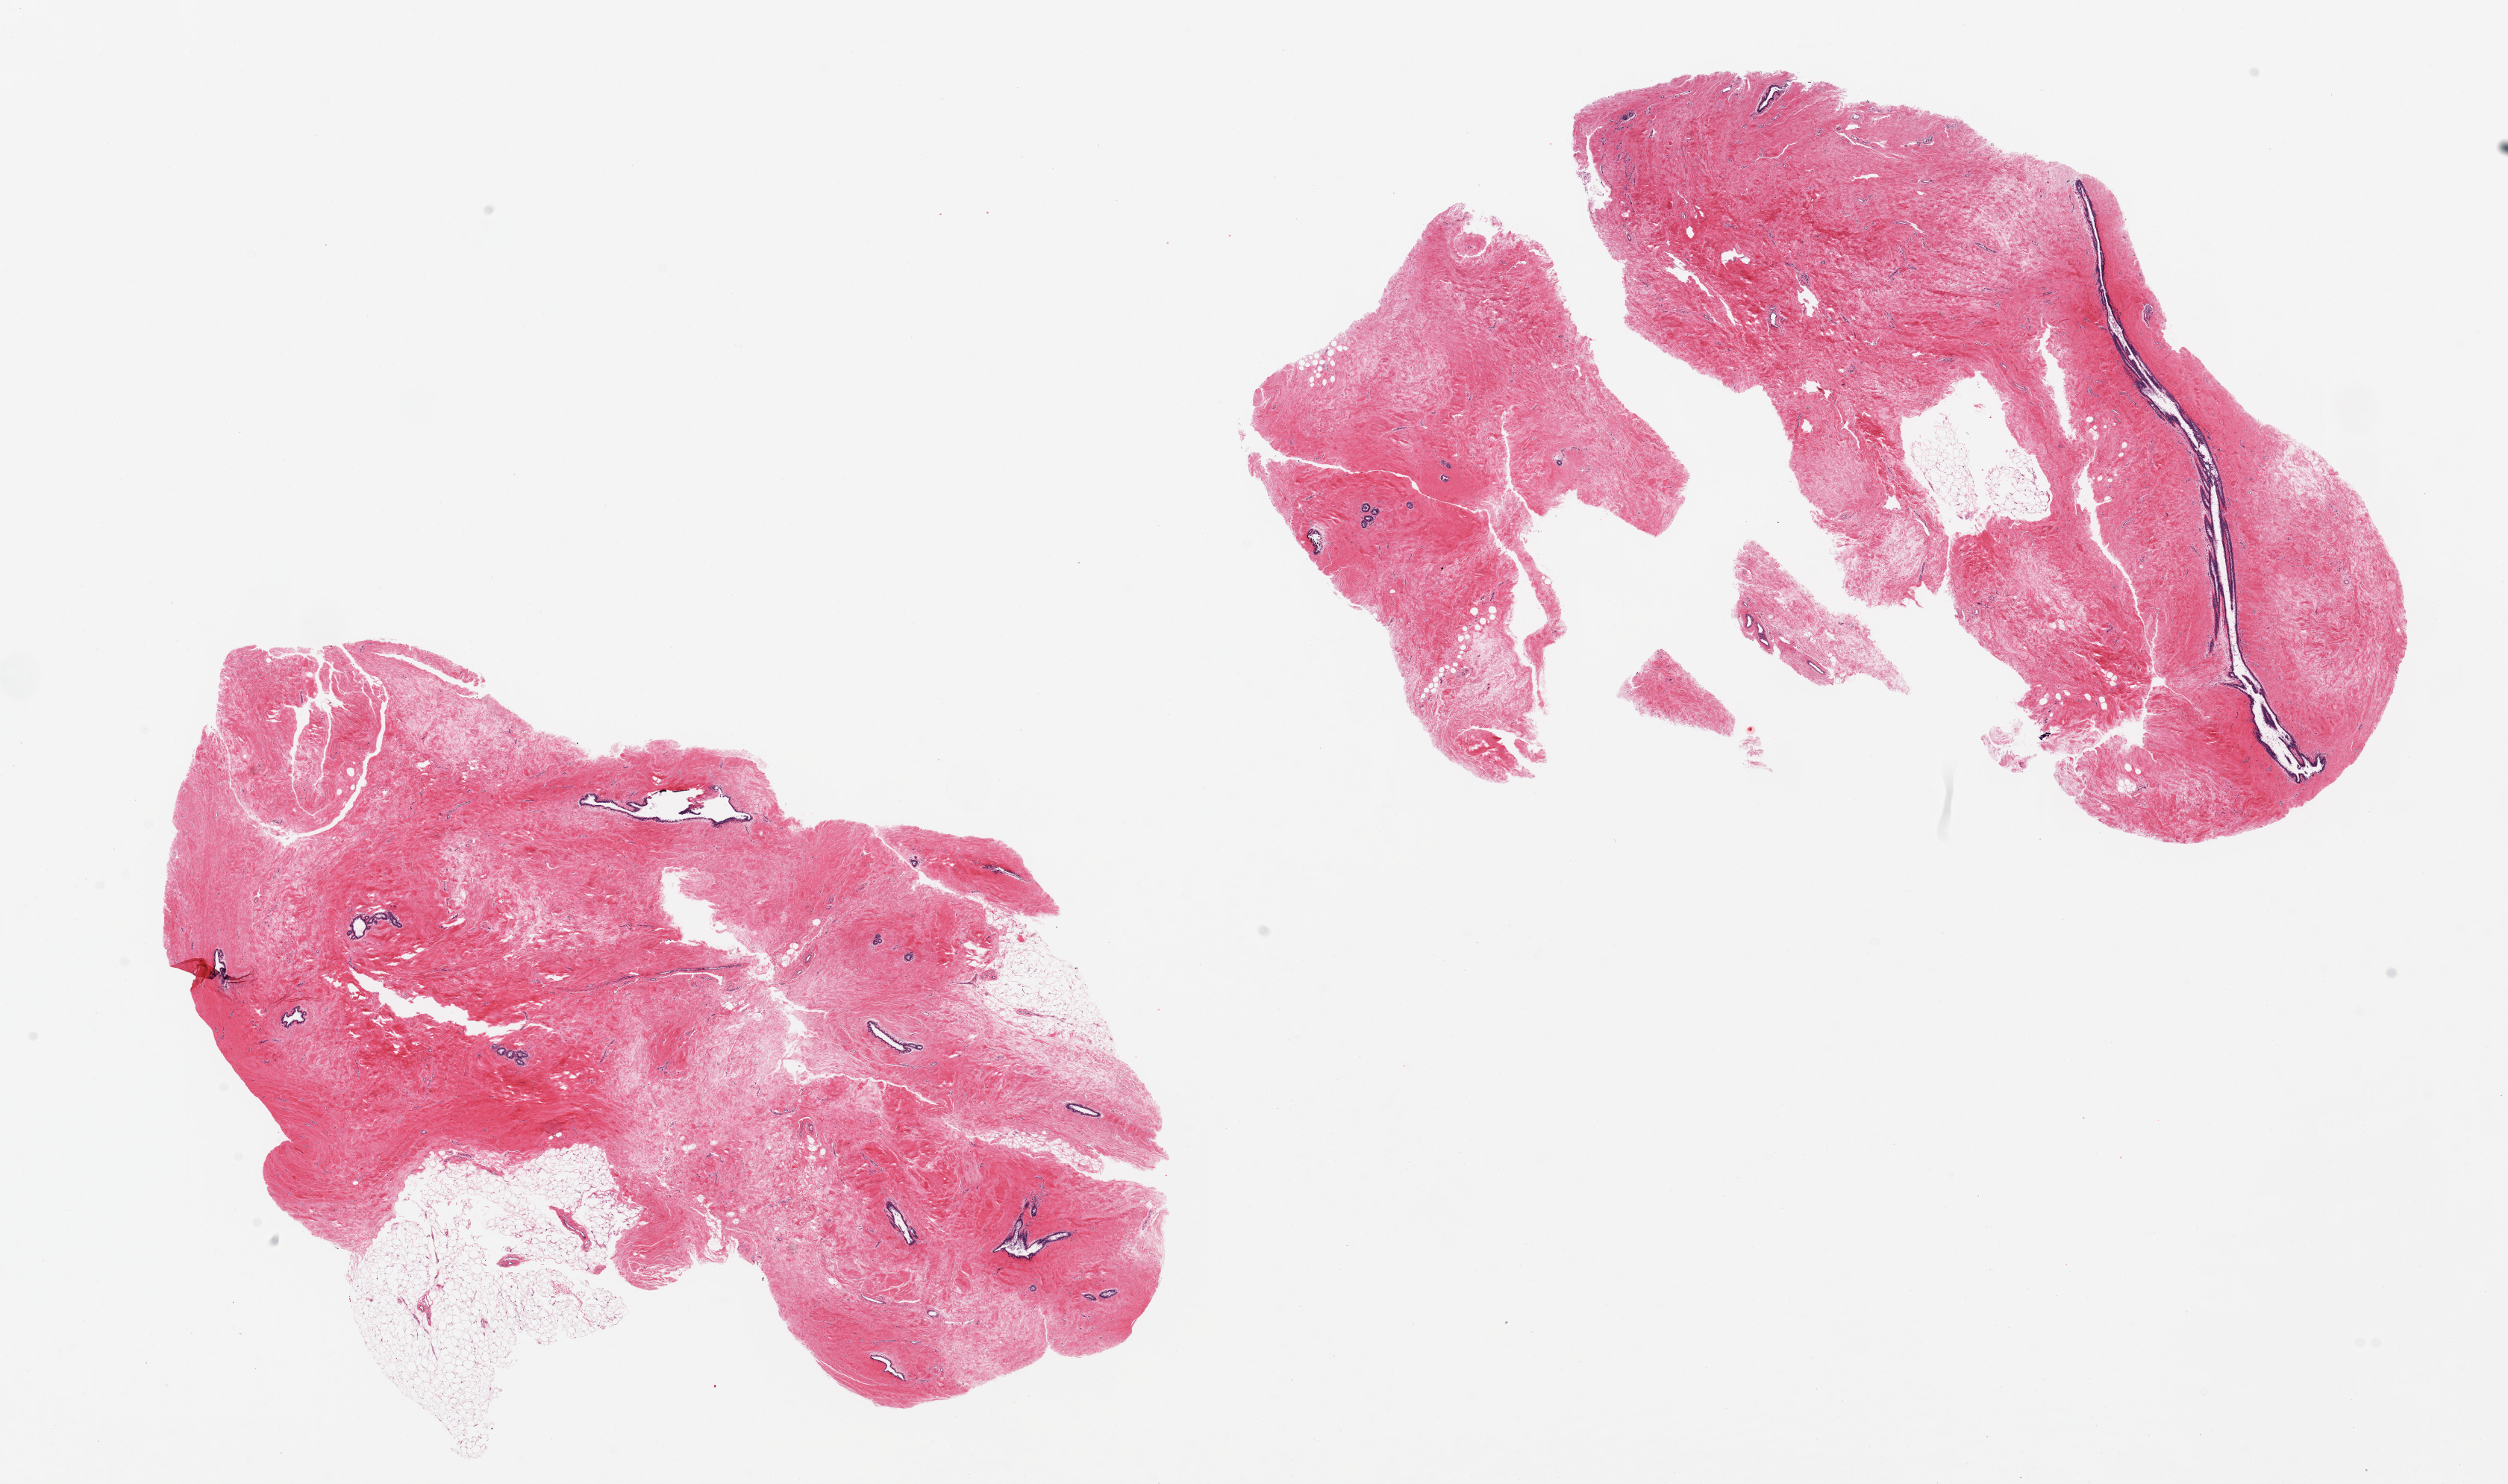
Digitized haematoxylin and eosin-stained section — low-resolution overview of the scanned area, about 26.6 x 15.7 mm (slide scanned at 20x), PAXgene-fixed paraffin-embedded (PFPE) section, section of breast (target tissue), donor tissue sample.
Review note (as recorded): 2 pieces, 12x6 & 10x4 mm; gynecomastia: ducts and fibrous tissue.